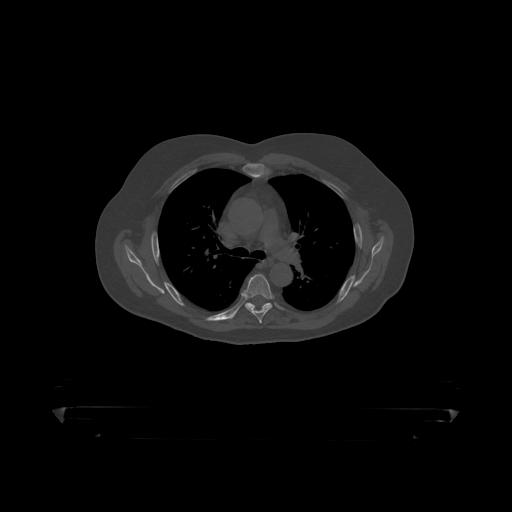
CT including the spine, one axial slice. Slice 315 of 390 in the series (ordered by position). 120 kVp. Bone window (W 1800 / L 400 HU). 1.25 mm slice thickness. 512 × 512 image matrix, field of view 650 × 650 mm. Male patient, age 60 years. From the clinical record (not read from this slice): primary cancer: prostate.
Structures marked on this image (semi-automatically segmented with operator editing):
- T5 vertebra: bounding box <243,274,274,319> (left, top, right, bottom; pixels)
- T6 vertebra: <245,303,273,309>